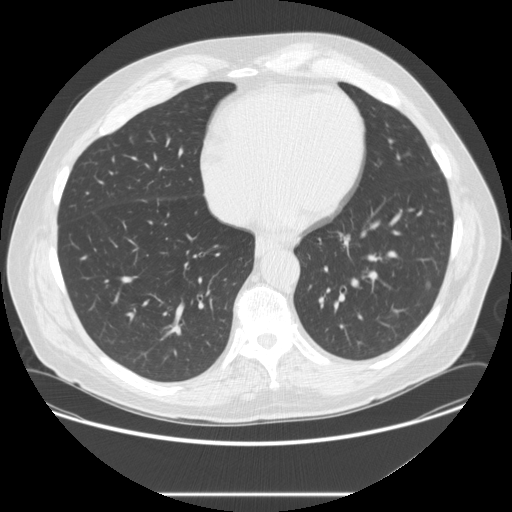
Axial slice from a low-dose chest CT screening exam; second annual screen; lung window (W 1500 / L -600 HU); 2.5 mm slice thickness; 512 × 512 image matrix, field of view 420 × 420 mm. Male participant, aged 67 years at enrolment. Current smoker at enrolment.
- Expert-annotated lung lesion, bounding box [x1, y1, x2, y2] px = [413, 265, 443, 297].
- Reader record for this screening exam (exam-level; its link to the box is not recorded): non-calcified nodule or mass ≥4 mm, left lower lobe, 4 × 4 mm, poorly defined margins, soft tissue attenuation, pre-existing on the prior screen: yes; interval growth: no.
- Official screen result: positive, other.
- Later outcome: lung cancer diagnosed 72 days after this screen — adenocarcinoma, NOS, left lower lobe, moderately differentiated (G2), stage IIA (AJCC 6th edition), 6 mm at pathology.